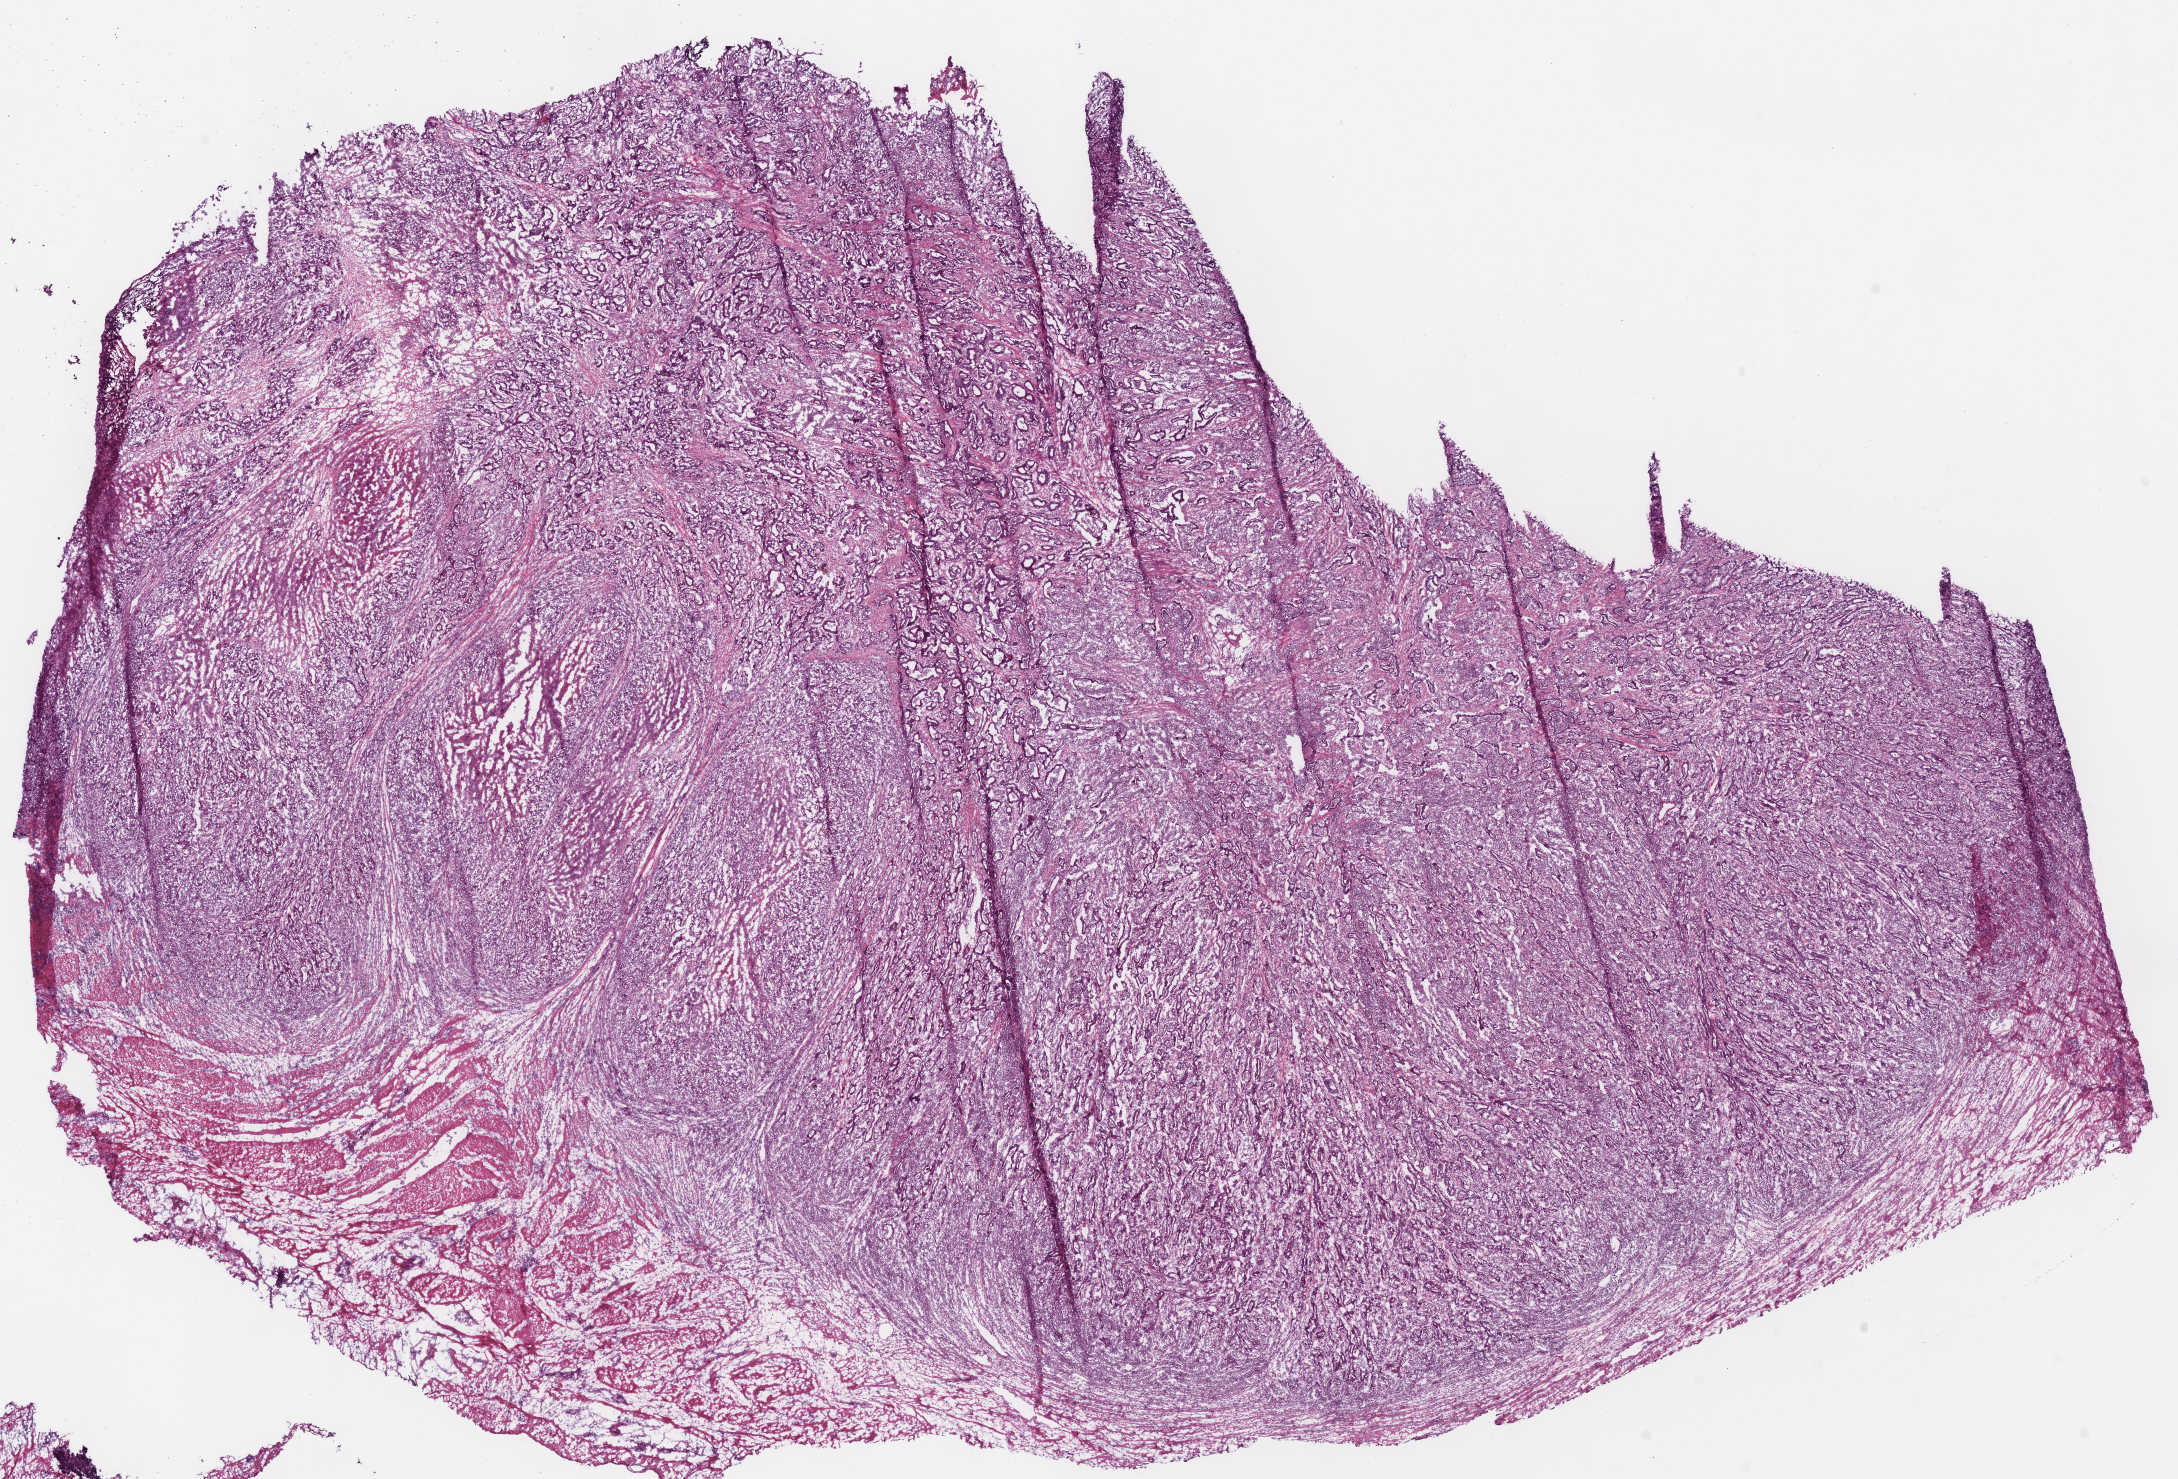
Digitized H&E tissue section (whole slide), a low-resolution overview of the entire scanned area, about 17.1 x 11.6 mm (acquisition: 40x scan); frozen section from the bottom of the tissue portion; primary tumour sample from the stomach. Patient: female, age at initial diagnosis 67 years. Histologic grade: G3 (poorly differentiated). Composition of this section per pathologist review: tumour cells 86%, tumour nuclei 65%, normal cells 14%, stromal cells 0%, necrosis 0%. Infiltration values recorded for this section: lymphocyte infiltration 5%, monocyte infiltration 2%, neutrophil infiltration 25%.
• TNM: T4b N3a M0
• diagnosis: Adenocarcinoma, NOS (gastric antrum)
• AJCC pathologic stage: IIIC (7th edition)